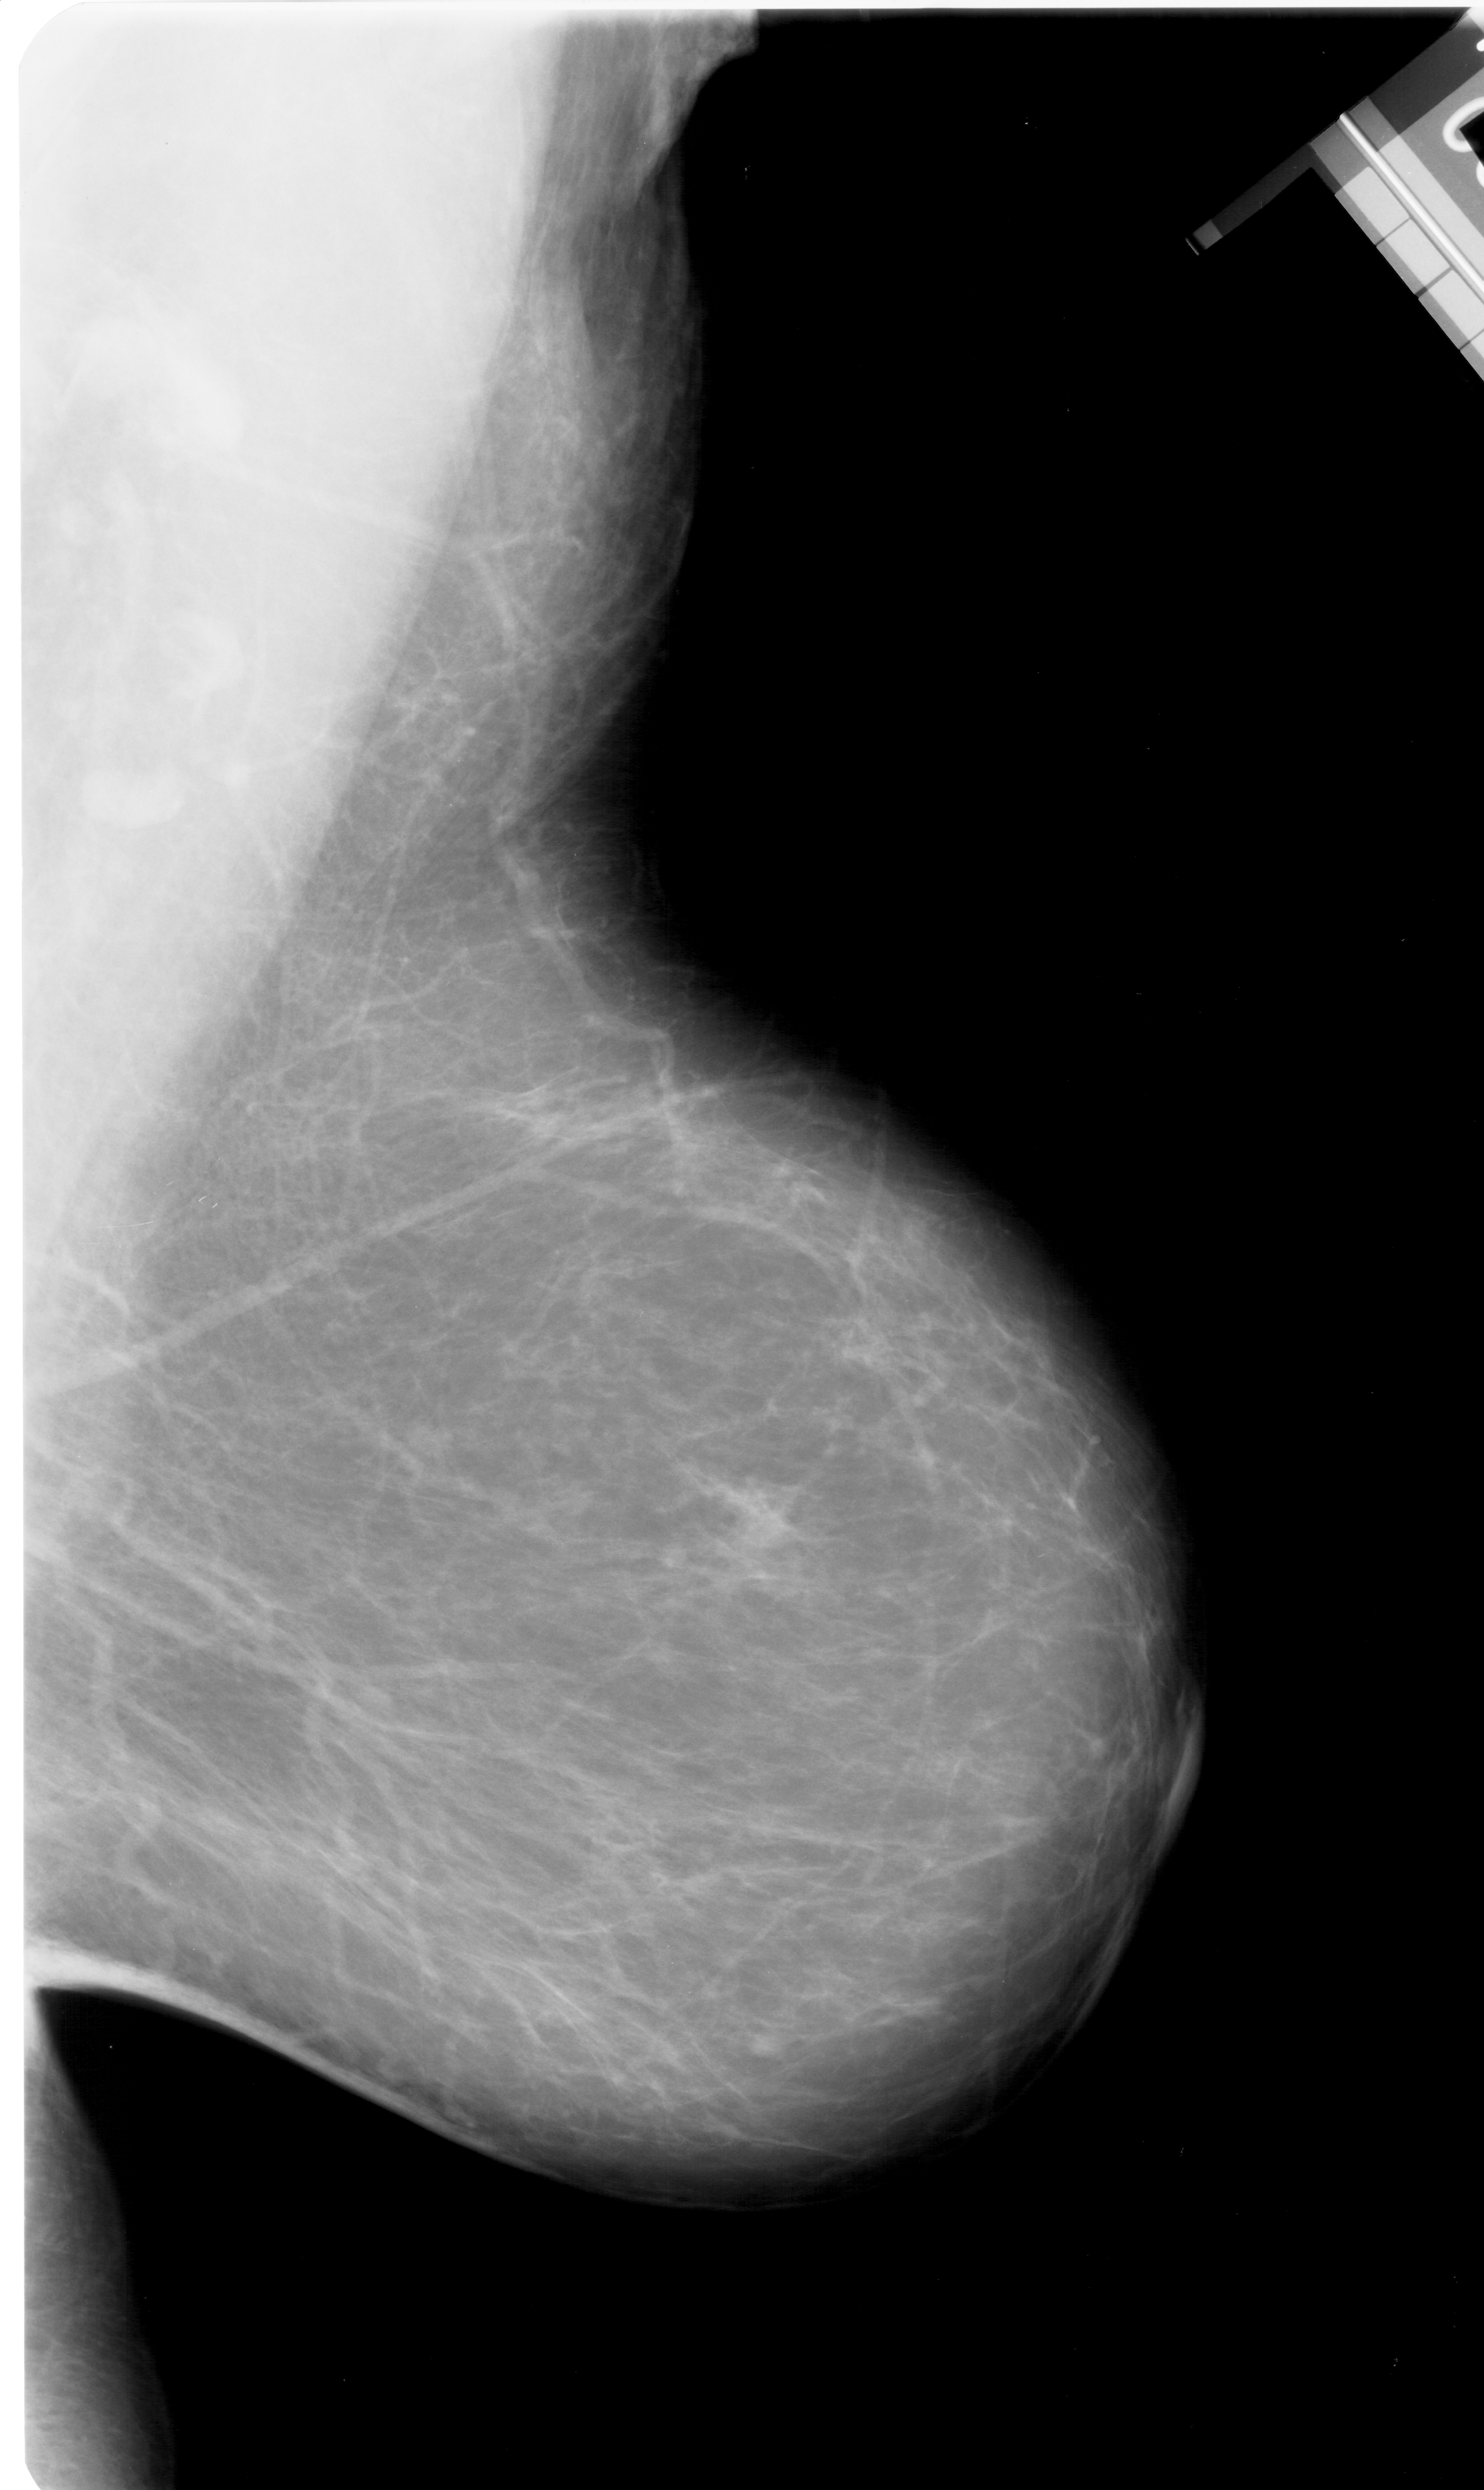
Digitized screen-film mammogram; right breast; mediolateral oblique (MLO) view; BI-RADS breast density category 2 (scale 1–4); 1484 × 2490 image matrix.
Marked abnormalities (boxes around the expert regions of interest):
- mass, shape lobulated, margins circumscribed; BI-RADS assessment category 4; subtlety rating 5 on a 1 (subtle) to 5 (obvious) scale; pathology (as recorded): malignant: bounding box [x1, y1, x2, y2] px = [726, 1483, 810, 1562]